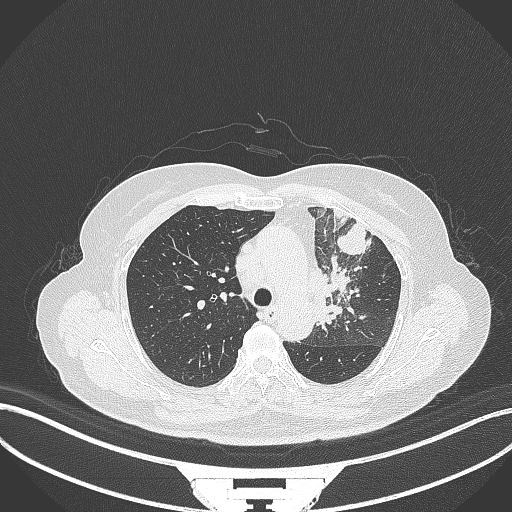
Chest CT, one axial slice; position 239 of 382 along the scan axis; reconstruction kernel B70f; 120 kVp; lung window (W 1500 / L -600 HU); 1 mm slice thickness; 512 × 512 image matrix, field of view 400 × 400 mm. Female patient, age 64 years. Case-level facts recorded for this patient, not image findings: clinical TNM (as recorded): T2a N2 M0.
Annotated regions visible in this slice (rectangle marked by the reading radiologist):
- lung tumour (recorded histology: adenocarcinoma): bounding box [x1, y1, x2, y2] px = [310, 254, 361, 335]
- lung tumour (recorded histology: adenocarcinoma): [333, 220, 373, 257]